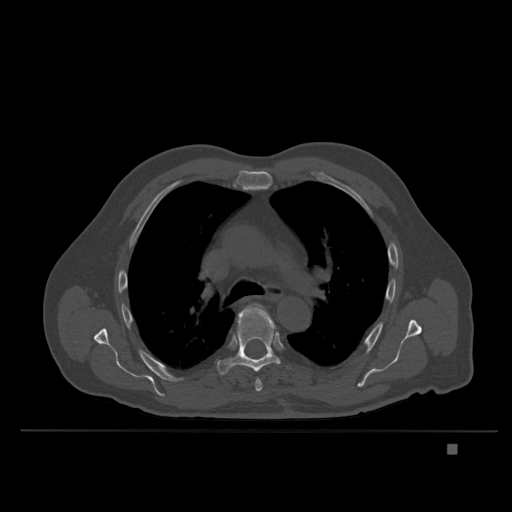
CT including the spine, one axial slice; position 262 of 435 along the scan axis; bone window (W 1800 / L 400 HU); 1.5 mm slice thickness; 512 × 512 image matrix. Patient: male, 73 years. From the clinical record (not read from this slice): primary cancer: skin.
Outlined on this slice (semi-automatically segmented with operator editing):
- T5 vertebra: box from (x=251, y=303) to (x=263, y=392) px
- T6 vertebra: (x=217, y=305)–(x=281, y=375)